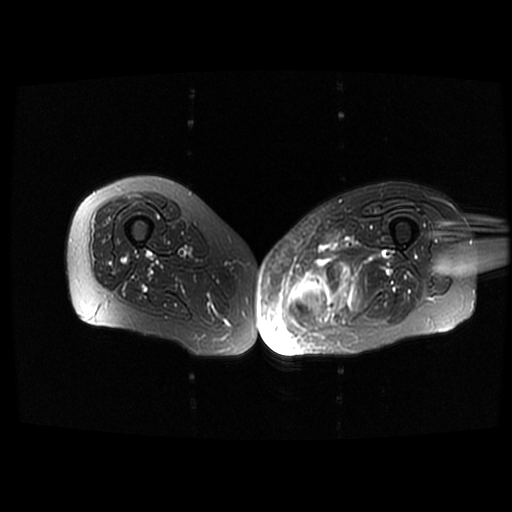
MRI of an extremity soft-tissue mass, one axial slice; T2-weighted fat-saturated; 6 mm slice thickness; 512 × 512 image matrix. Female patient. Case-level facts recorded for this patient, not image findings: histological type: pleomorphic leiomyosarcoma; grade: high; site of the primary tumour: left thigh.
Annotated regions visible in this slice (outlined manually by an expert reader):
- gross tumour volume including surrounding oedema: box from (x=287, y=259) to (x=350, y=328) px